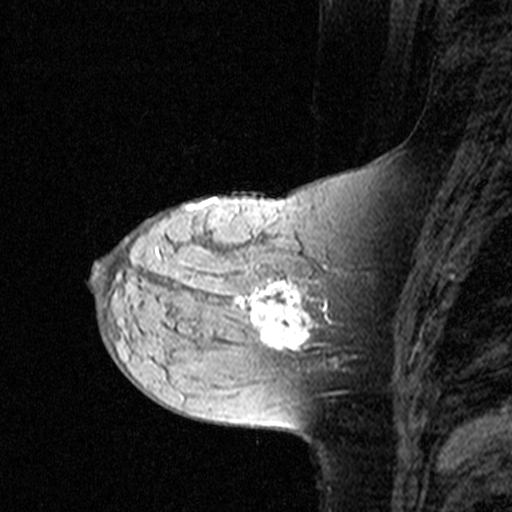
Breast MRI (dynamic contrast-enhanced), one sagittal slice. Position 14 of 44 along the scan axis. Dynamic contrast-enhanced study with each time point stored as its own series, time point 2 of 3 at this slice position (early post-contrast, ordered by acquisition time). 1.5 T. TE 4.5 ms, TR 11 ms. 3 mm slice thickness. 512 × 512 image matrix. Female patient, age 44 years. From the clinical record (not read from this slice): setting: breast cancer imaged before/during neoadjuvant chemotherapy; receptor status: triple-negative.
Structures marked on this image (semi-automatic segmentation, software-assisted and operator-edited):
- analysis volume of interest (the breast-tissue region the enhancement analysis was run in; not a lesion): box from (x=142, y=208) to (x=349, y=363) px
- tumour enhancement mask (voxels above the 90 % enhancement threshold inside the analysis volume of interest): (x=256, y=280)–(x=327, y=350)